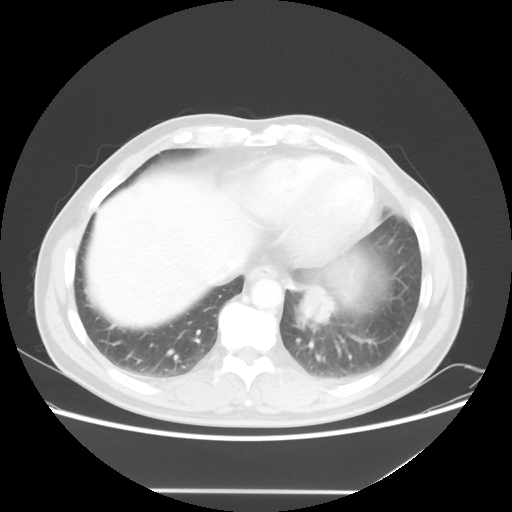
Chest CT, one axial slice. Position 15 of 56 along the scan axis. 120 kVp. Lung window (W 1500 / L -600 HU). 5 mm slice thickness. 512 × 512 image matrix. Patient: male, 61 years. Case-level facts recorded for this patient, not image findings: clinical TNM (as recorded): T1c N0 M0.
Outlined on this slice (rectangle marked by the reading radiologist):
- lung tumour (recorded histology: adenocarcinoma): box from (x=295, y=277) to (x=339, y=324) px